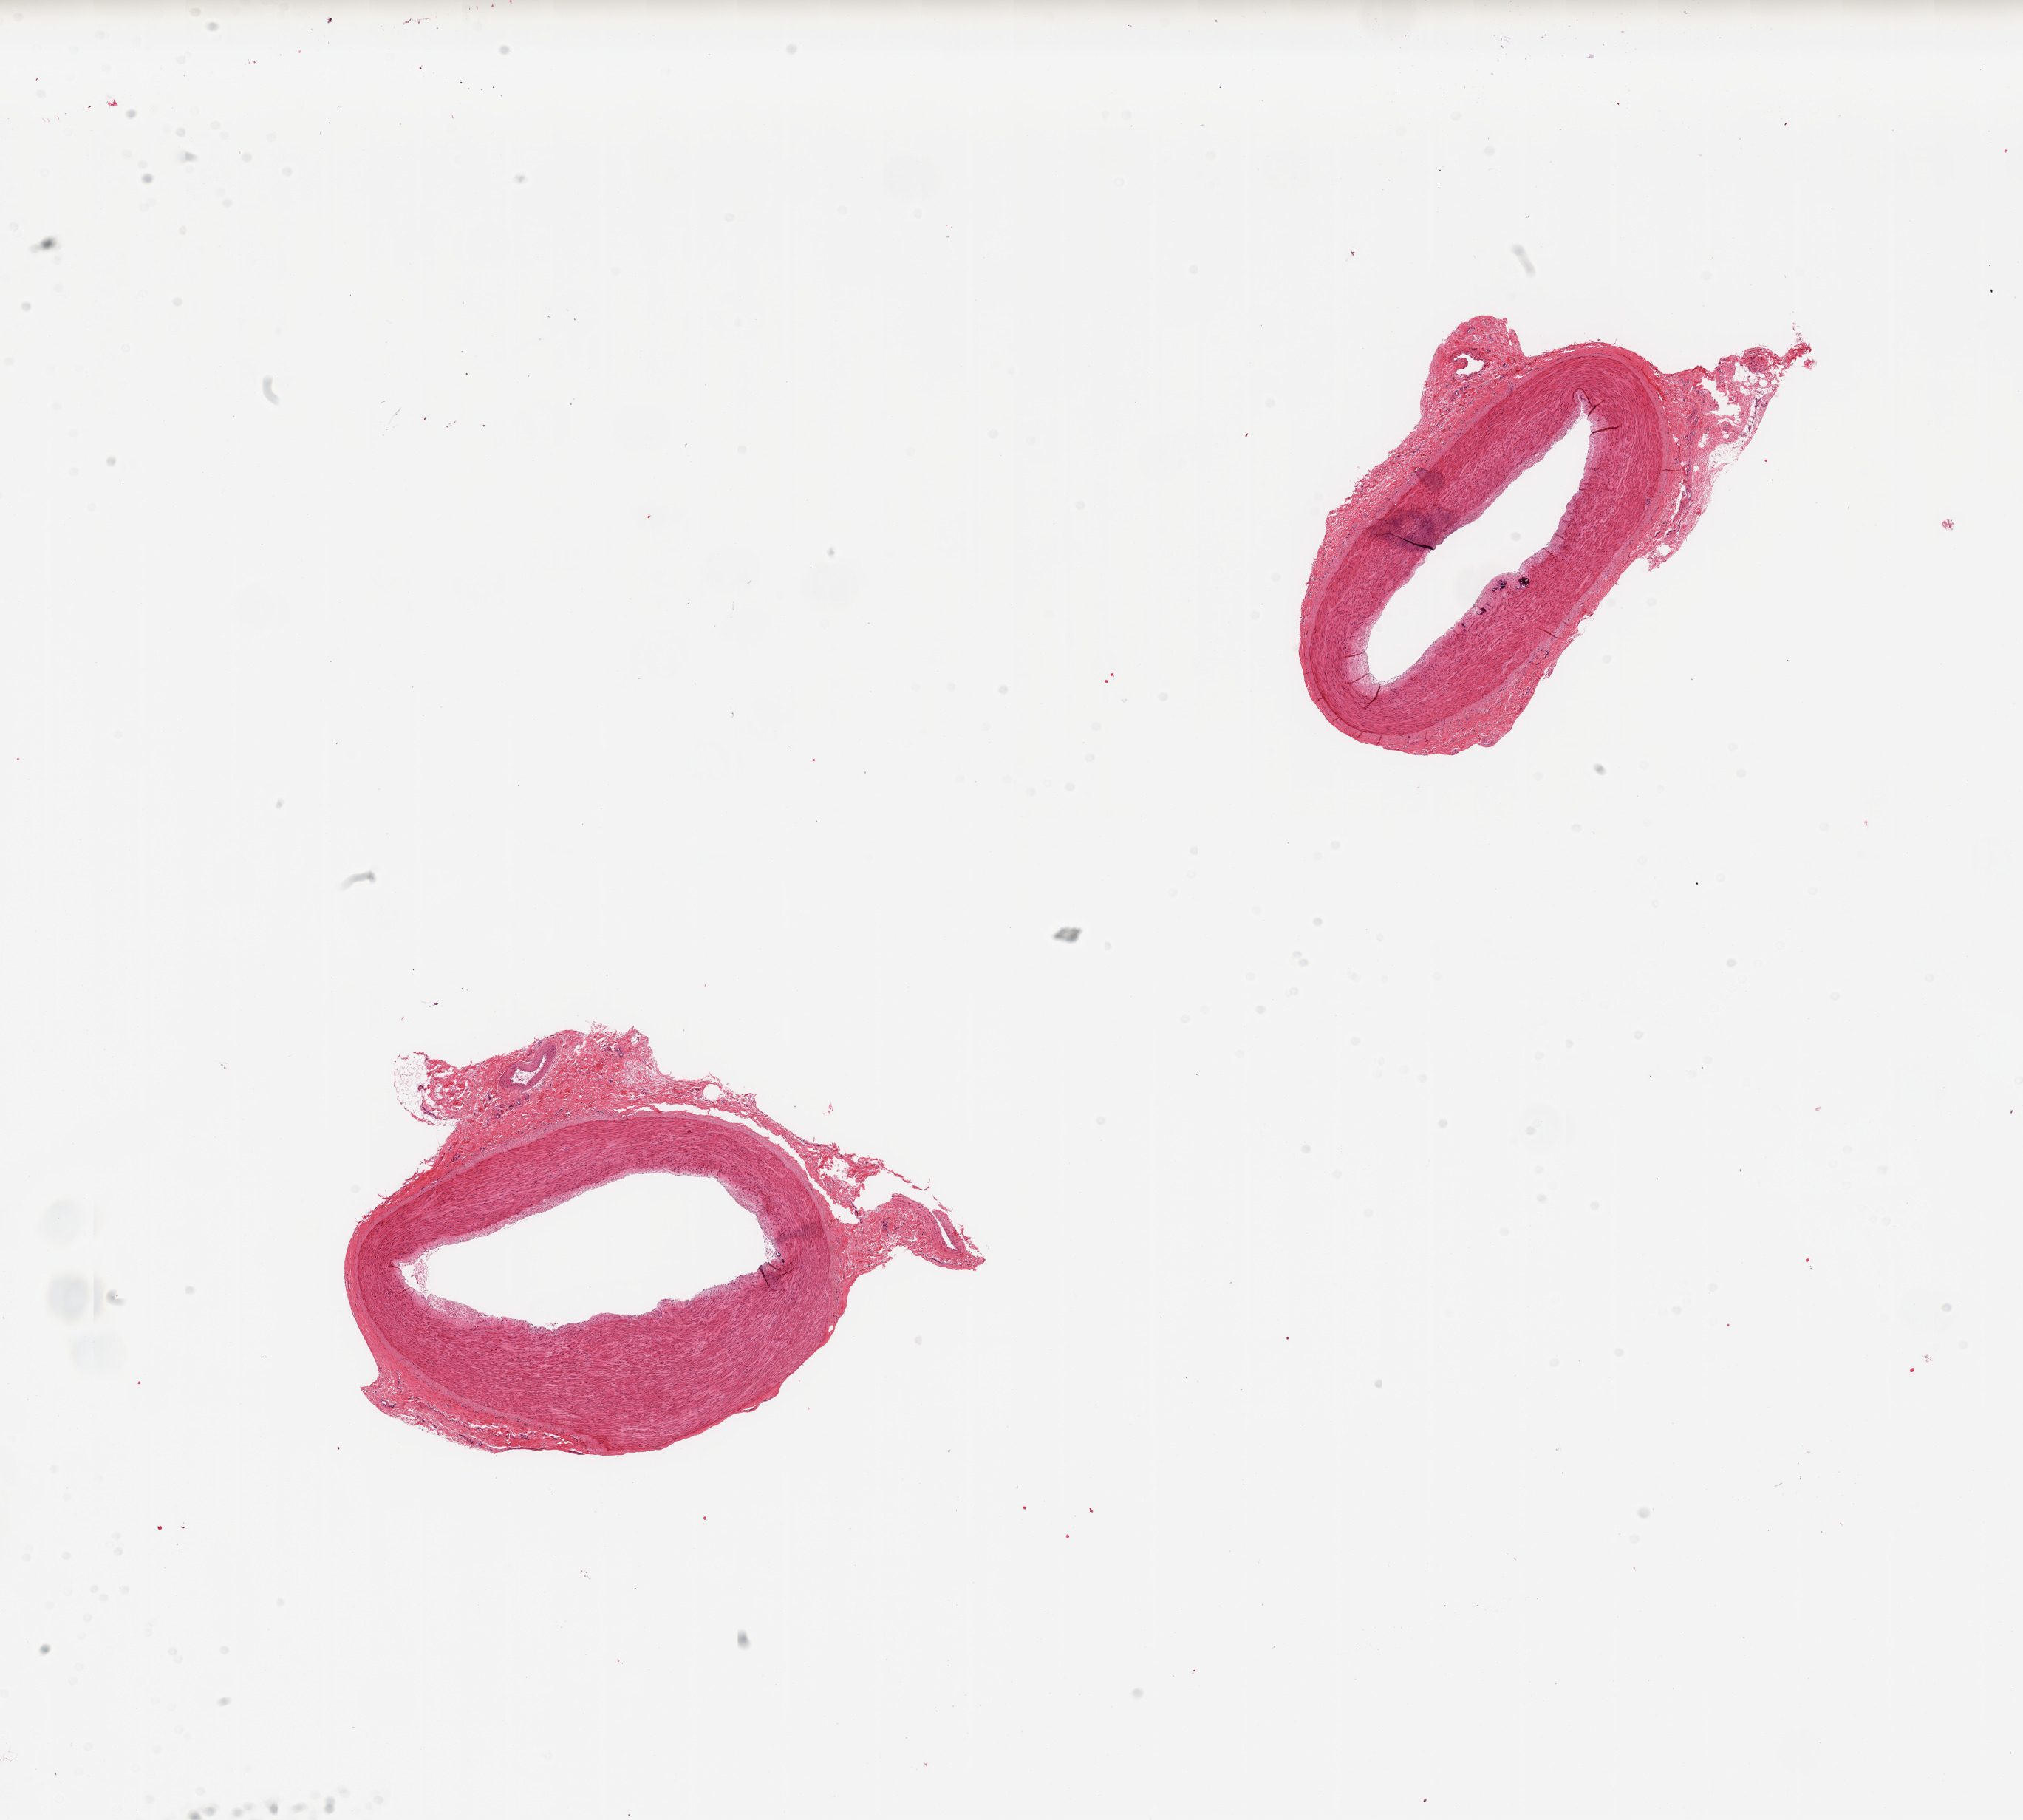
Hematoxylin and eosin (H&E) whole-slide image, brightfield, a low-resolution overview of the entire scanned area, about 21.7 x 19.5 mm (slide scanned at 20x). PAXgene-fixed, paraffin-embedded tissue. Sampled site (target tissue): tibial artery. Donor tissue sample. Male donor.
Pathologist's review note for this sample: 2 pieces, trace adherent fibrous tissue.